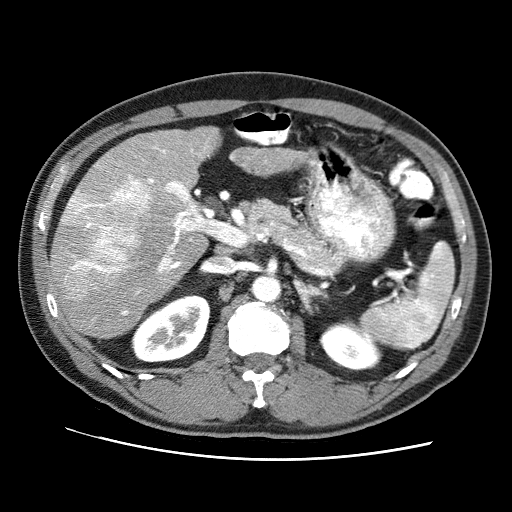
Contrast-enhanced abdominal CT (liver protocol), one axial slice; position 42 of 71 along the scan axis; 120 kVp; soft-tissue window (W 400 / L 40 HU); 2.5 mm slice thickness; 512 × 512 image matrix, field of view 360 × 360 mm. Case-level facts recorded for this patient, not image findings: diagnosis: hepatocellular carcinoma (patient treated with transarterial chemoembolisation; whether this scan precedes or follows treatment is not stated here); TNM stage (as recorded): Stage-II; Child-Pugh class: A; tumour size: 4.6 cm.
Annotated regions visible in this slice (semi-automatic segmentation, software-assisted and operator-edited):
- liver parenchyma outside the tumour (the mass and vessels are separate outlines, so this box may not span the whole liver): bounding box (x1, y1, x2, y2) in pixels: (48, 126, 303, 338)
- mass: (59, 181, 153, 302)
- liver vessels: (70, 147, 207, 315)